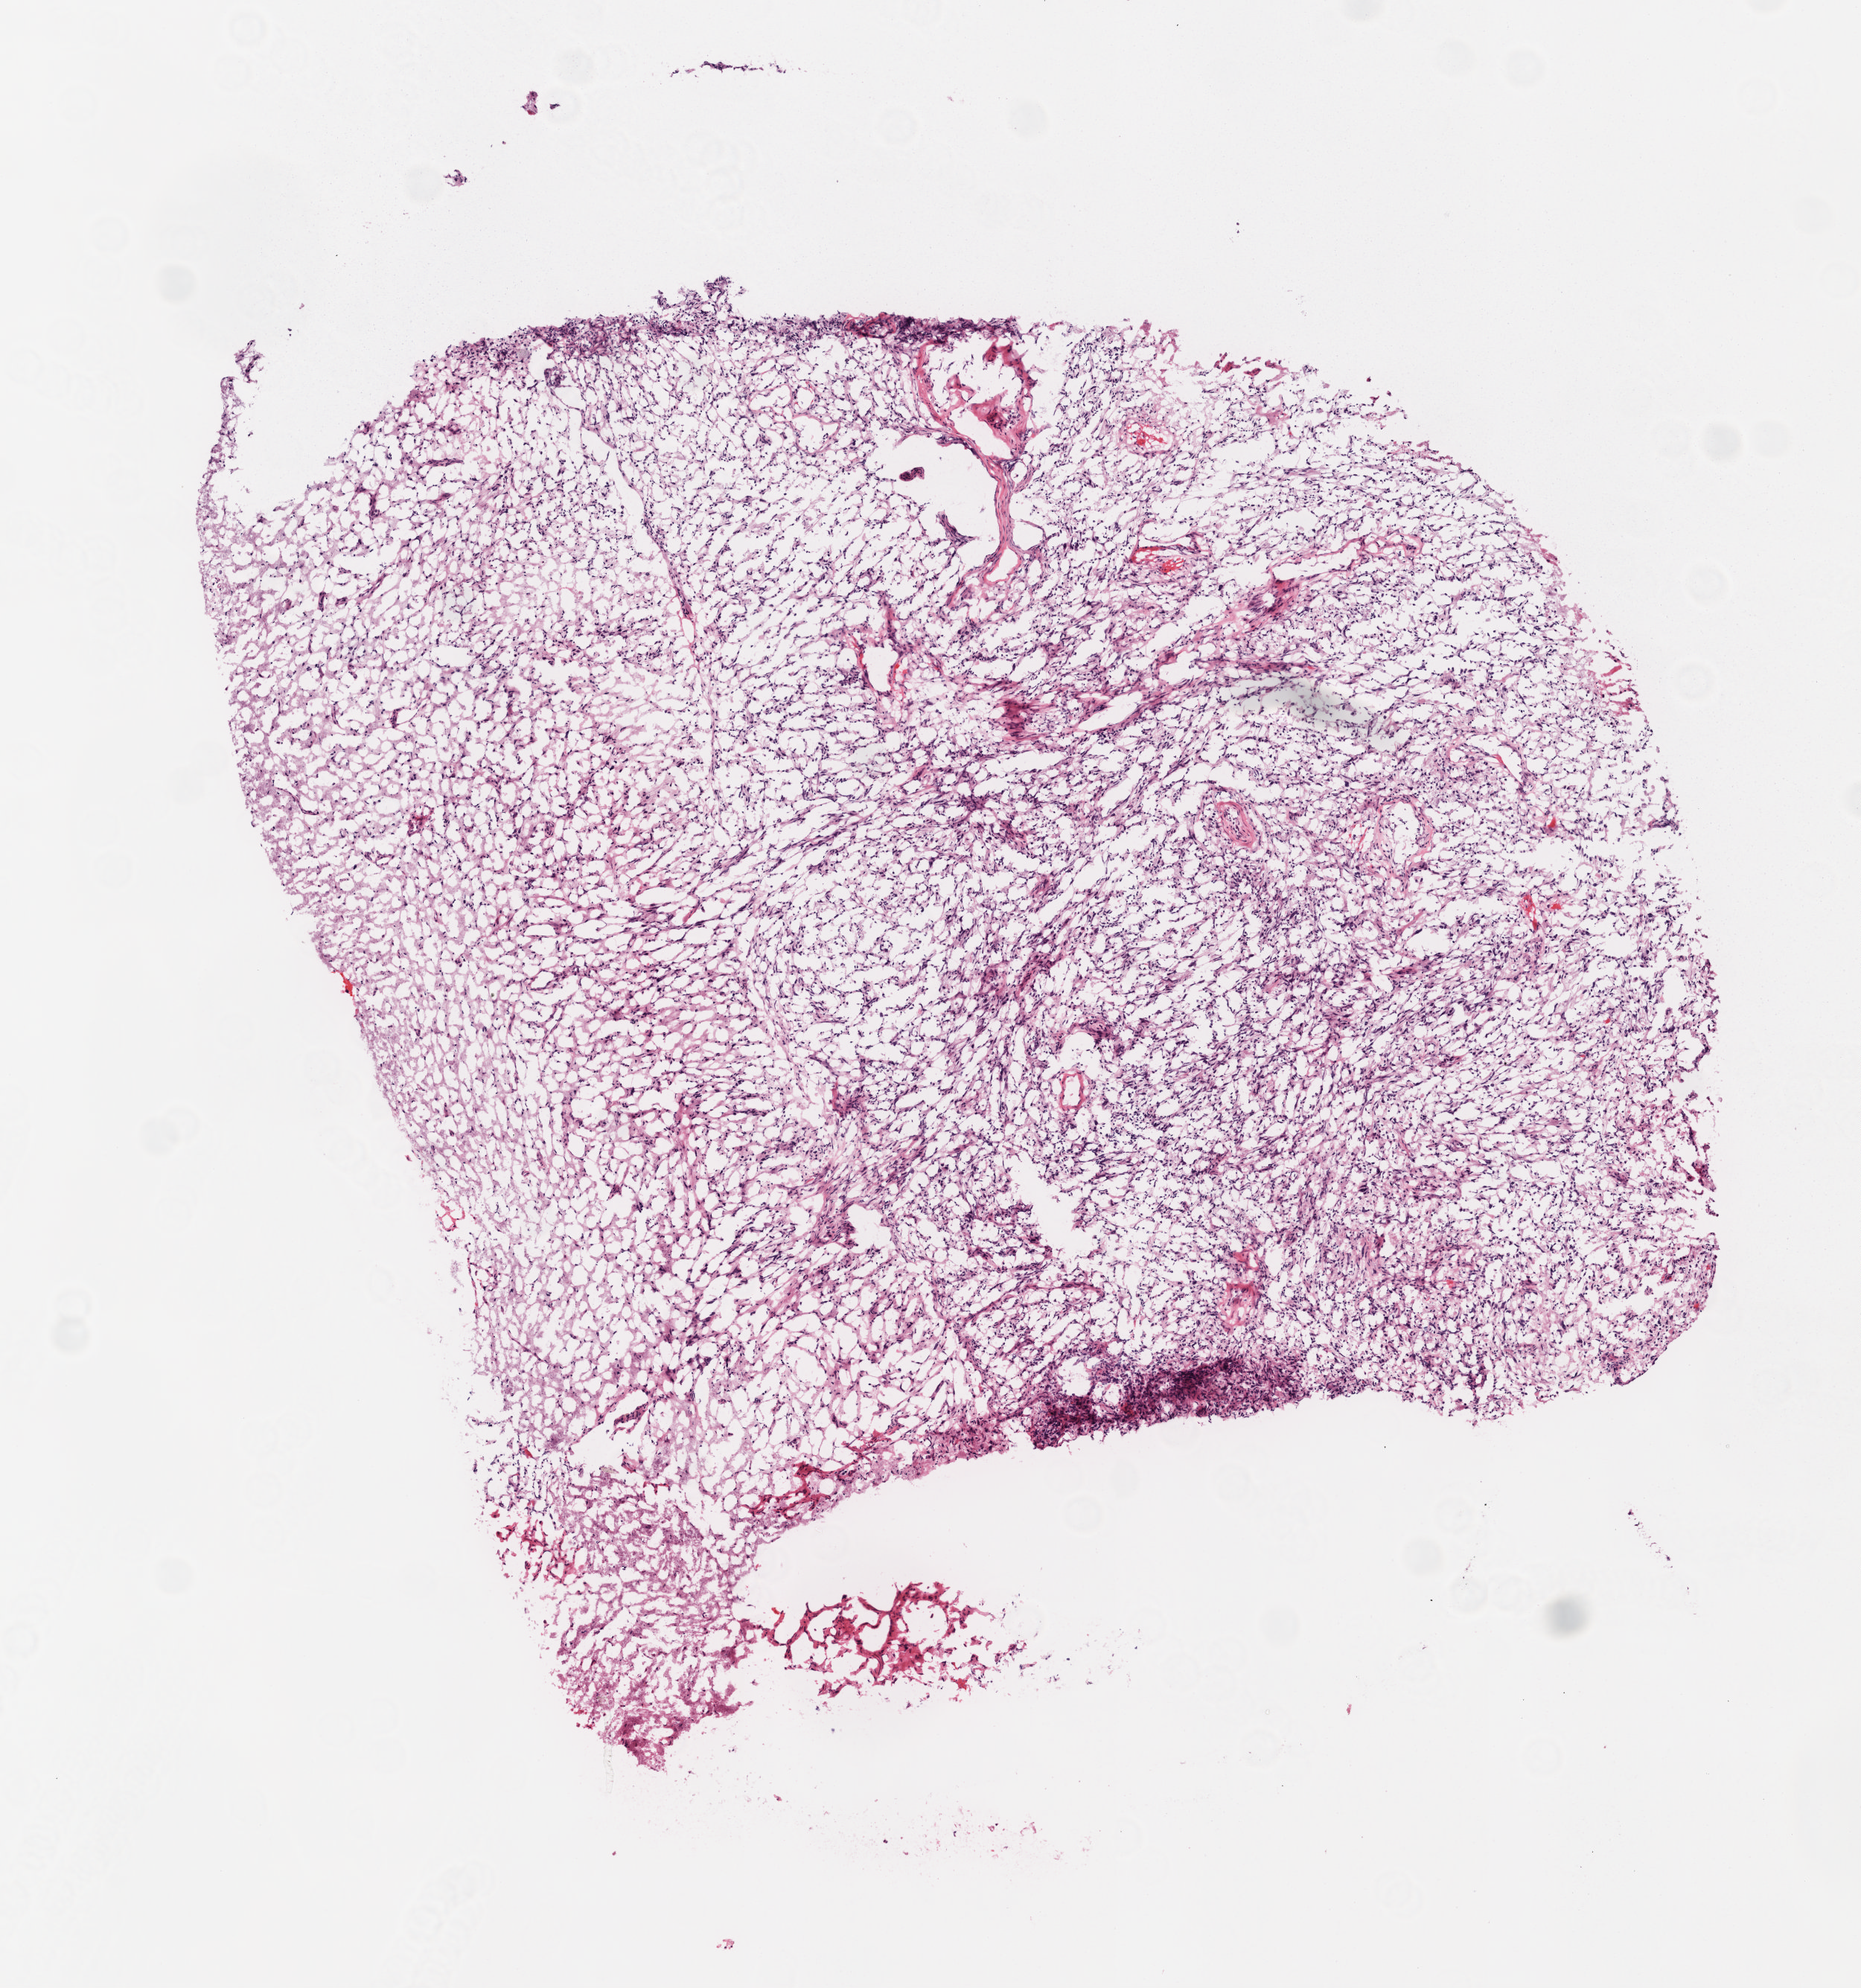
H&E whole-slide image — low-resolution overview of the scanned area, about 5.0 x 5.4 mm (acquisition: 20x scan). Frozen section from the top of the tissue portion. Brain, primary tumour sample. Male, age 36 years at initial diagnosis. Composition of this section per pathologist review: tumour cells 95%, tumour nuclei 80%, normal cells 0%, stromal cells 0%, necrosis 5%.
* diagnosis: Glioblastoma